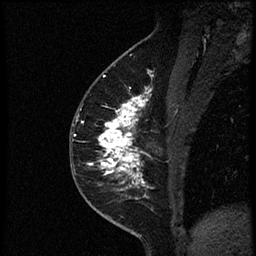
Breast MRI (dynamic contrast-enhanced), one sagittal slice; slice 31 of 56 in the series (ordered by position); dynamic contrast-enhanced study with each time point stored as its own series, time point 2 of 4 at this slice position (early post-contrast, ordered by acquisition time); 1.5 T; TE 4.2 ms, TR 18.9 ms; 2 mm slice thickness; 256 × 256 image matrix, field of view 200 × 200 mm. Female patient. Case-level facts recorded for this patient, not image findings: setting: breast cancer imaged before/during neoadjuvant chemotherapy; receptor status: HER2-positive.
Annotated regions visible in this slice (semi-automatic segmentation, software-assisted and operator-edited):
- analysis volume of interest (the breast-tissue region the enhancement analysis was run in; not a lesion): bounding box [x1, y1, x2, y2] px = [78, 85, 174, 189]
- tumour enhancement mask (voxels above the 100 % enhancement threshold inside the analysis volume of interest): [89, 90, 153, 189]